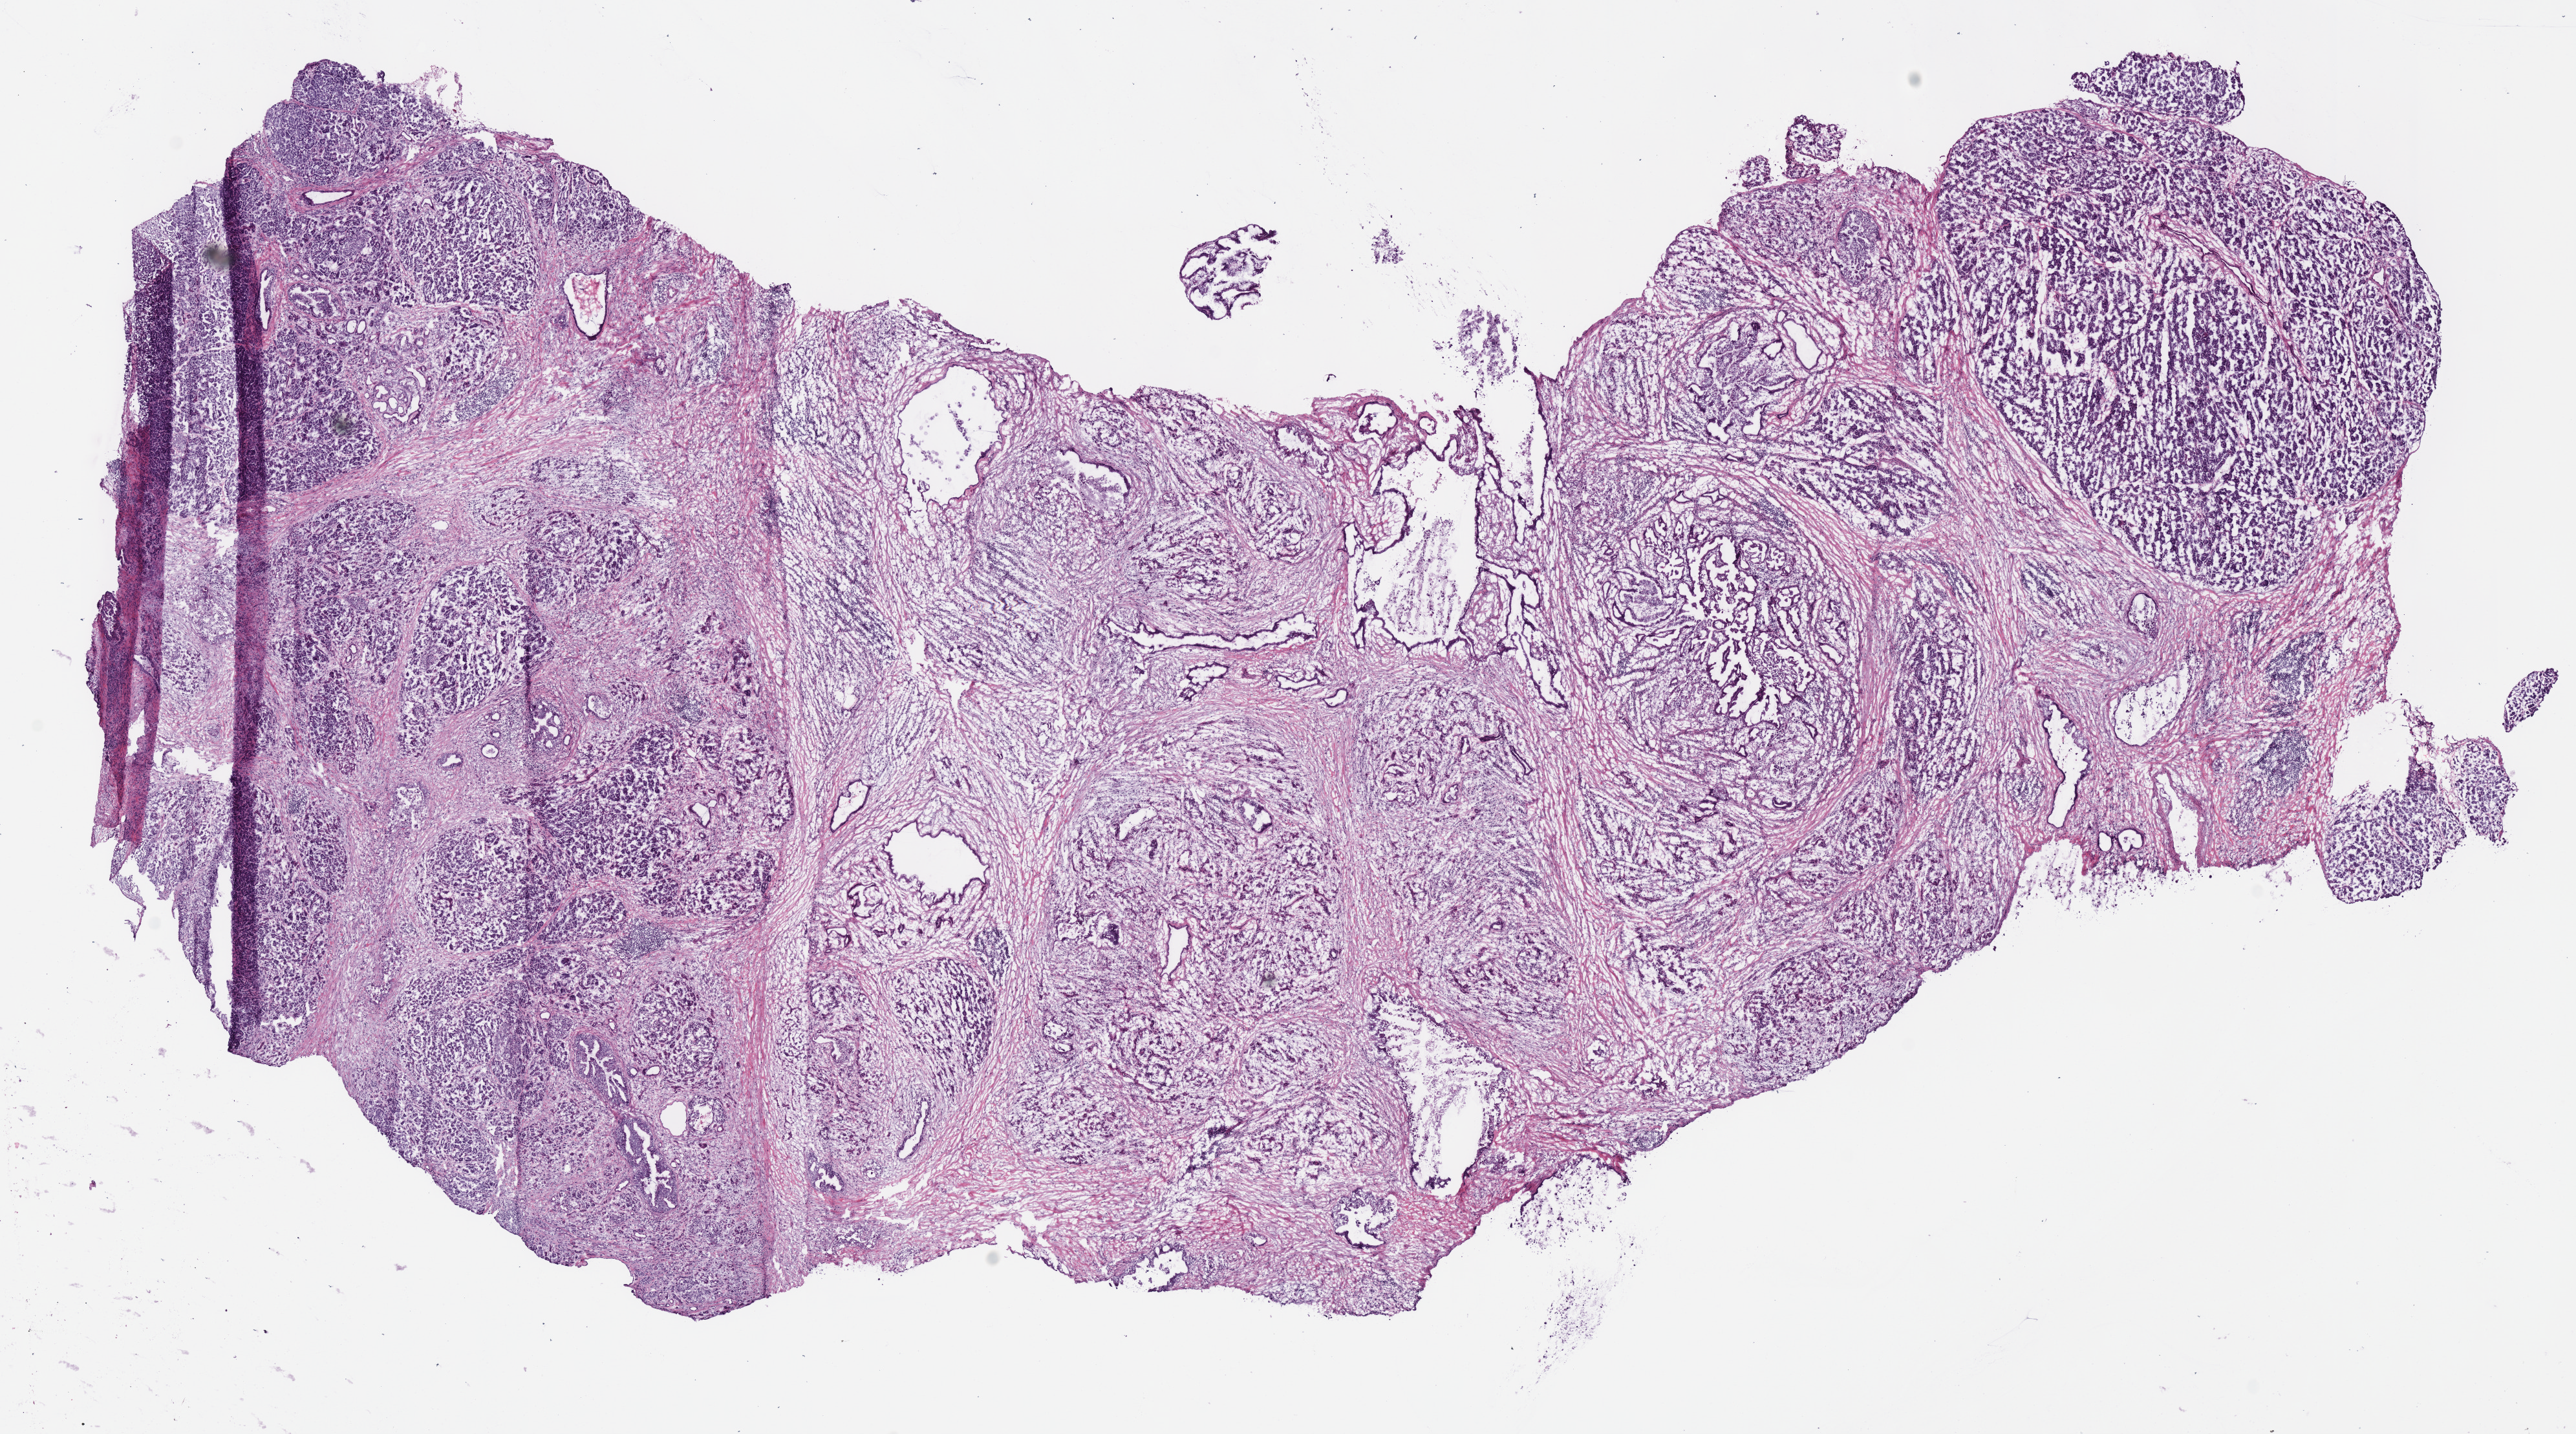
Whole-slide histology image, H&E — low-resolution overview of the scanned area, about 15.7 x 8.7 mm (acquisition: 40x scan), frozen section, primary tumour sample from the pancreas. Female, age 49 years at initial diagnosis. Histologic grade: G1 (well differentiated). Pathologist review of this section (percent, as recorded): tumour cells 55%, tumour nuclei 60%, normal cells 25%, stromal cells 15%, necrosis 5%.
Pathologic diagnosis: Infiltrating duct carcinoma, NOS. Lymph nodes positive (case pathology): 7 of 11 examined. AJCC pathologic stage: IIB (7th edition). TNM: T3 N1 M0.